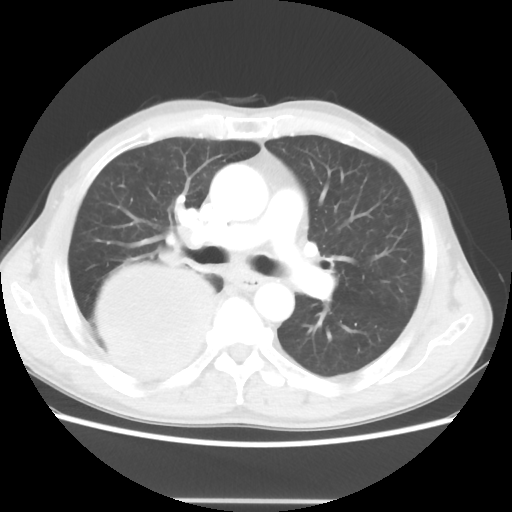
Chest CT, one axial slice. Position 29 of 48 along the scan axis. 100 kVp. Lung window (W 1500 / L -600 HU). 5 mm slice thickness. 512 × 512 image matrix, field of view 361 × 361 mm. Male patient, age 66 years. From the clinical record (not read from this slice): clinical TNM (as recorded): T4 N1 M1; histopathological grade: G3.
Annotated regions visible in this slice (rectangle marked by the reading radiologist):
- lung tumour (recorded histology: small cell carcinoma): bounding box <99,258,220,396> (left, top, right, bottom; pixels)